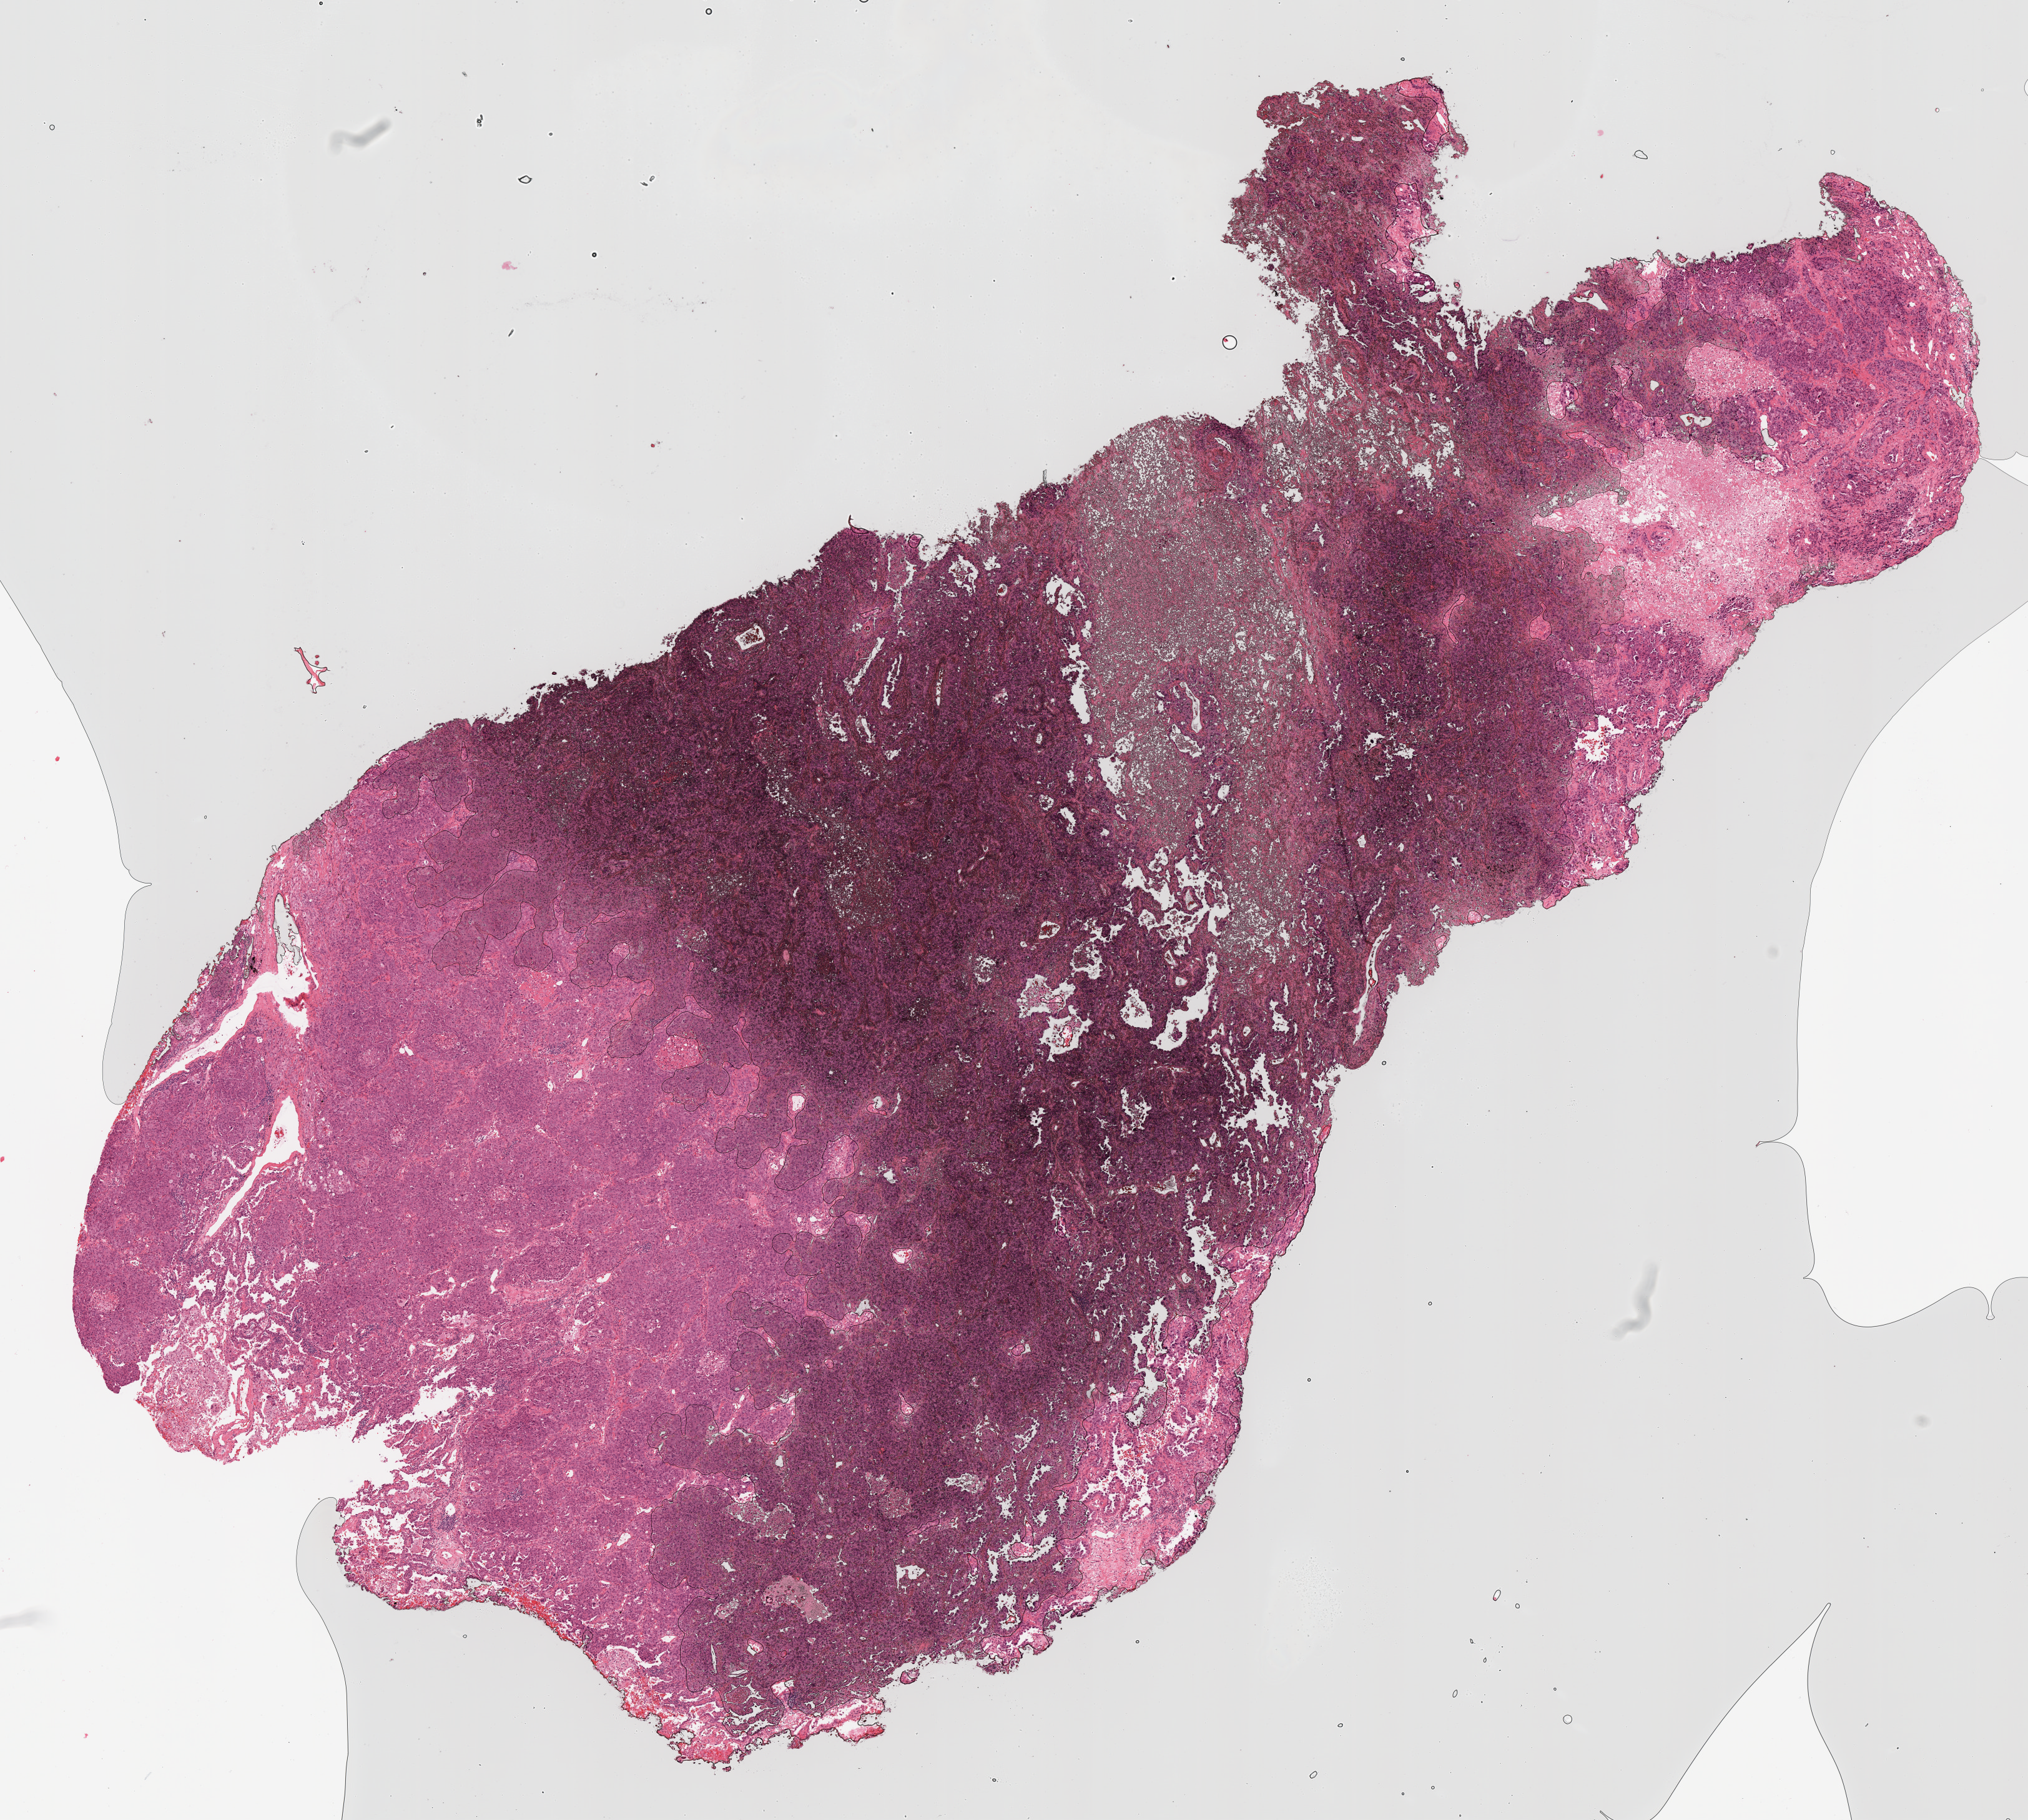
Digitized Hematoxylin and eosin (H&E) stained tissue section (whole slide) — whole scanned area (about 13.0 x 11.7 mm, acquisition: 20x scan) shown as a low-resolution overview. Formalin-fixed paraffin-embedded (FFPE) diagnostic section. Lung, primary tumour sample. Patient sex: male.
• AJCC pathologic stage: IIIA
• TNM: T2 N2 M0
• histologic diagnosis: Adenocarcinoma, NOS
• laterality: right